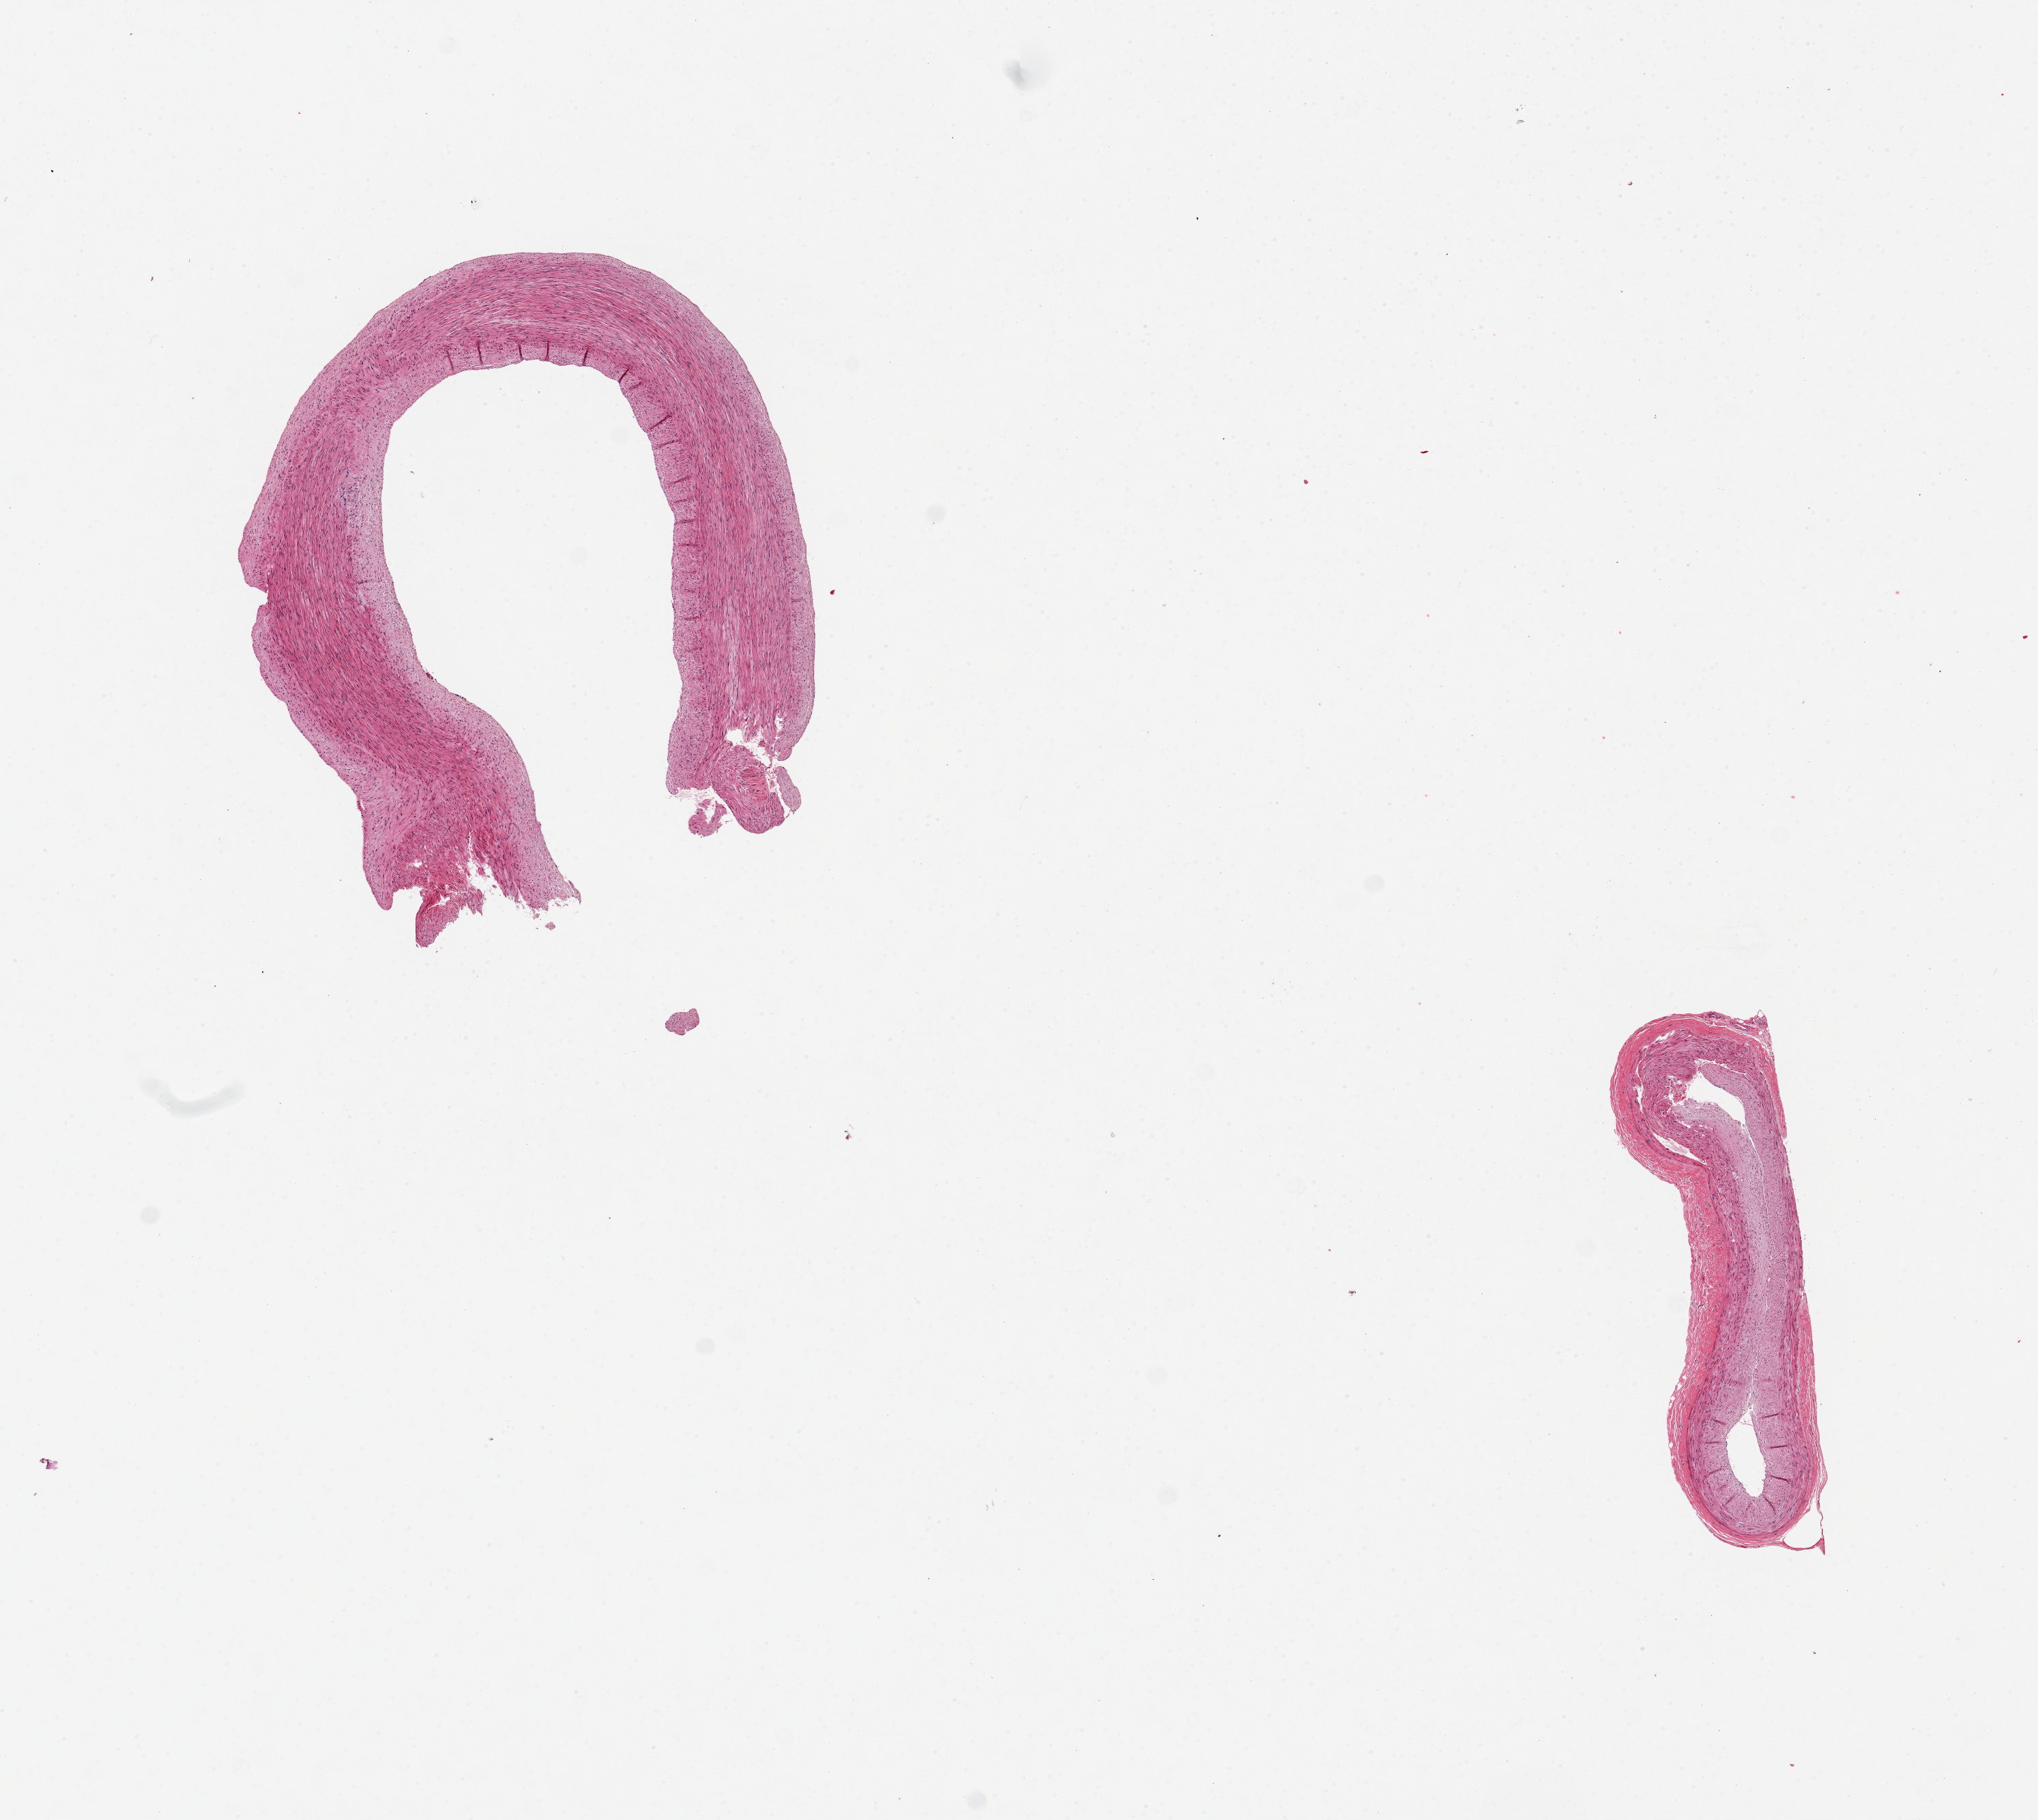
Digitized H&E-stained section, shown as a low-resolution overview of the whole scanned area (about 11.8 x 10.5 mm, acquisition: 20x scan), PAXgene-fixed paraffin-embedded (PFPE) section, sampled site (target tissue): coronary artery, tissue donor sample. Donor: male.
- review note (as recorded): 2 pieces. Uniform plaques, not severe